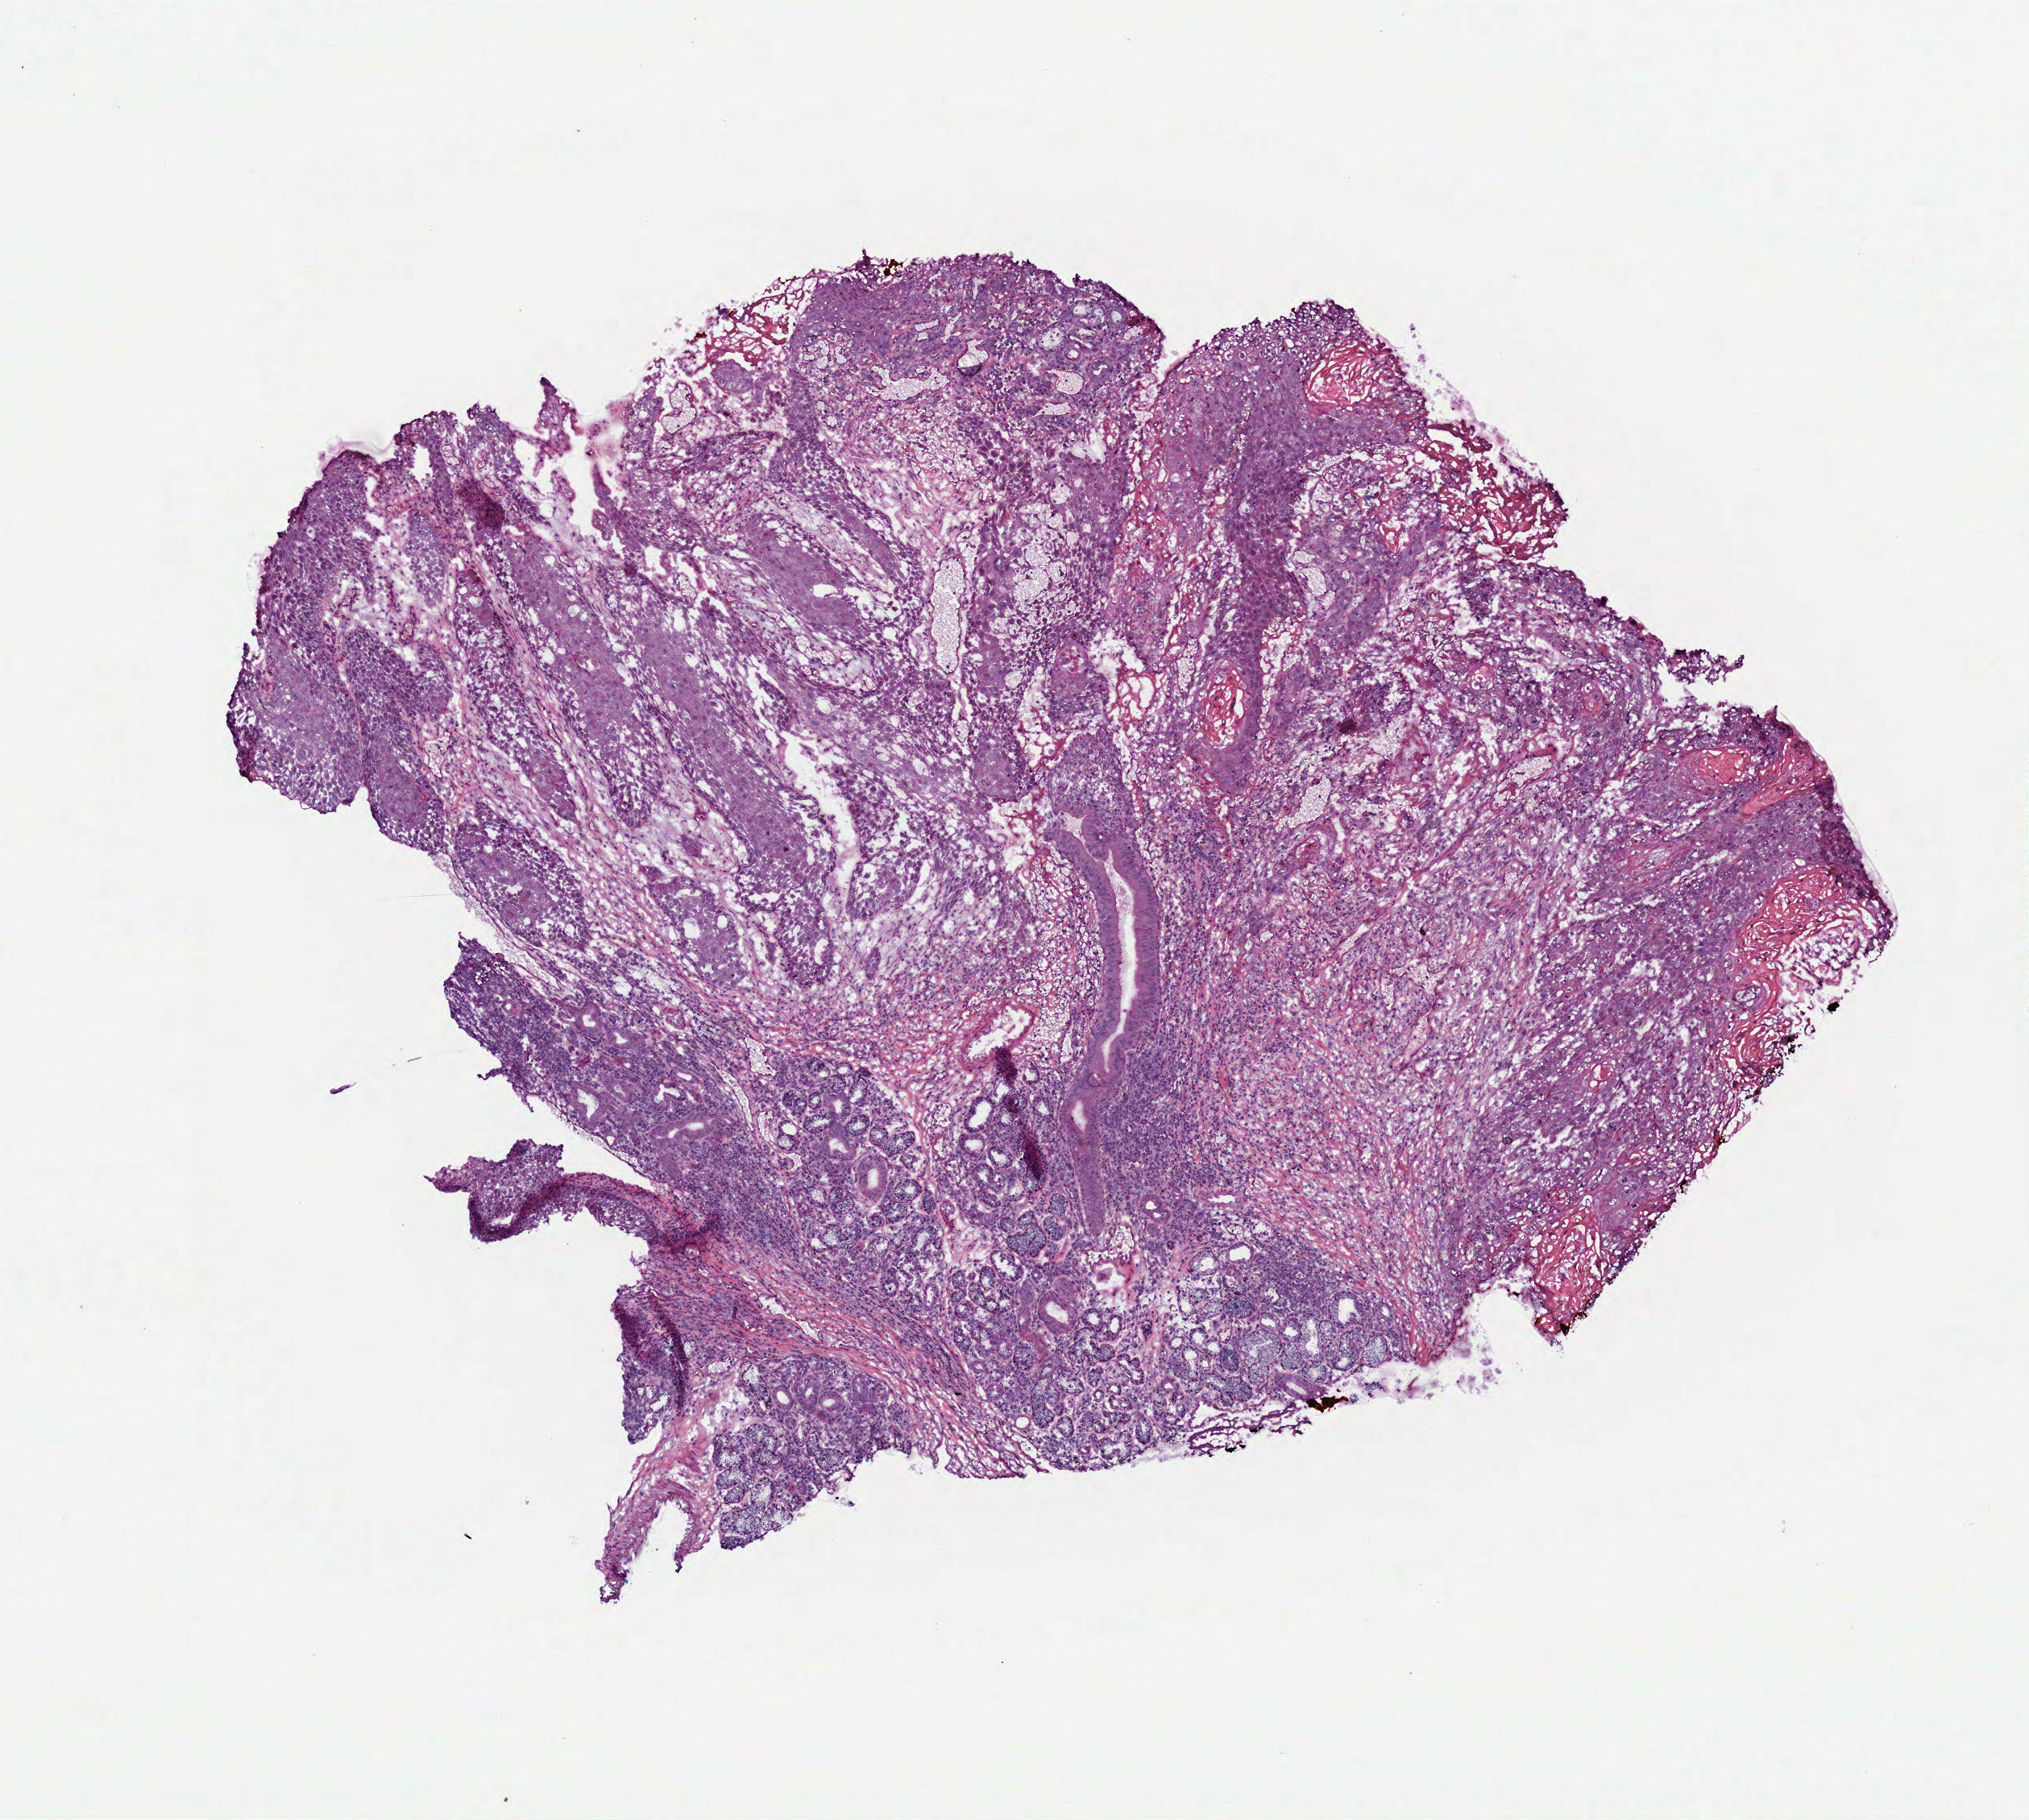
Digitized H&E-stained tissue section (whole slide), low-resolution overview of the scanned area, about 5.1 x 4.6 mm (from a 40x scan). Frozen section from the top of the tissue portion. Head and neck, primary tumour sample. Male patient; age at initial diagnosis 62 years. Histologic grade: G1 (well differentiated). Pathologist review of this section (percent, as recorded): tumour cells 75%, tumour nuclei 60%, normal cells 5%, stromal cells 20%, necrosis 0%.
Pathologic diagnosis: Squamous cell carcinoma, keratinizing, NOS (floor of mouth, NOS). AJCC pathologic stage: II.